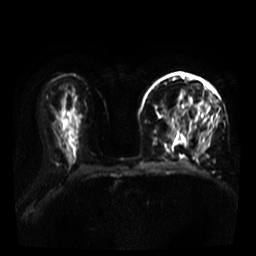
Breast MRI, one axial slice. Position 19 of 39 along the scan axis. Diffusion-weighted series; image 2 of 4 stored at this slice position (different b-values; order by instance number). 3 T. 256 × 256 image matrix, field of view 320 × 320 mm. Female patient.
Structures marked on this image (outlined manually by an expert reader):
- tumour on diffusion-weighted imaging: bounding box [x1, y1, x2, y2] px = [189, 99, 202, 113]